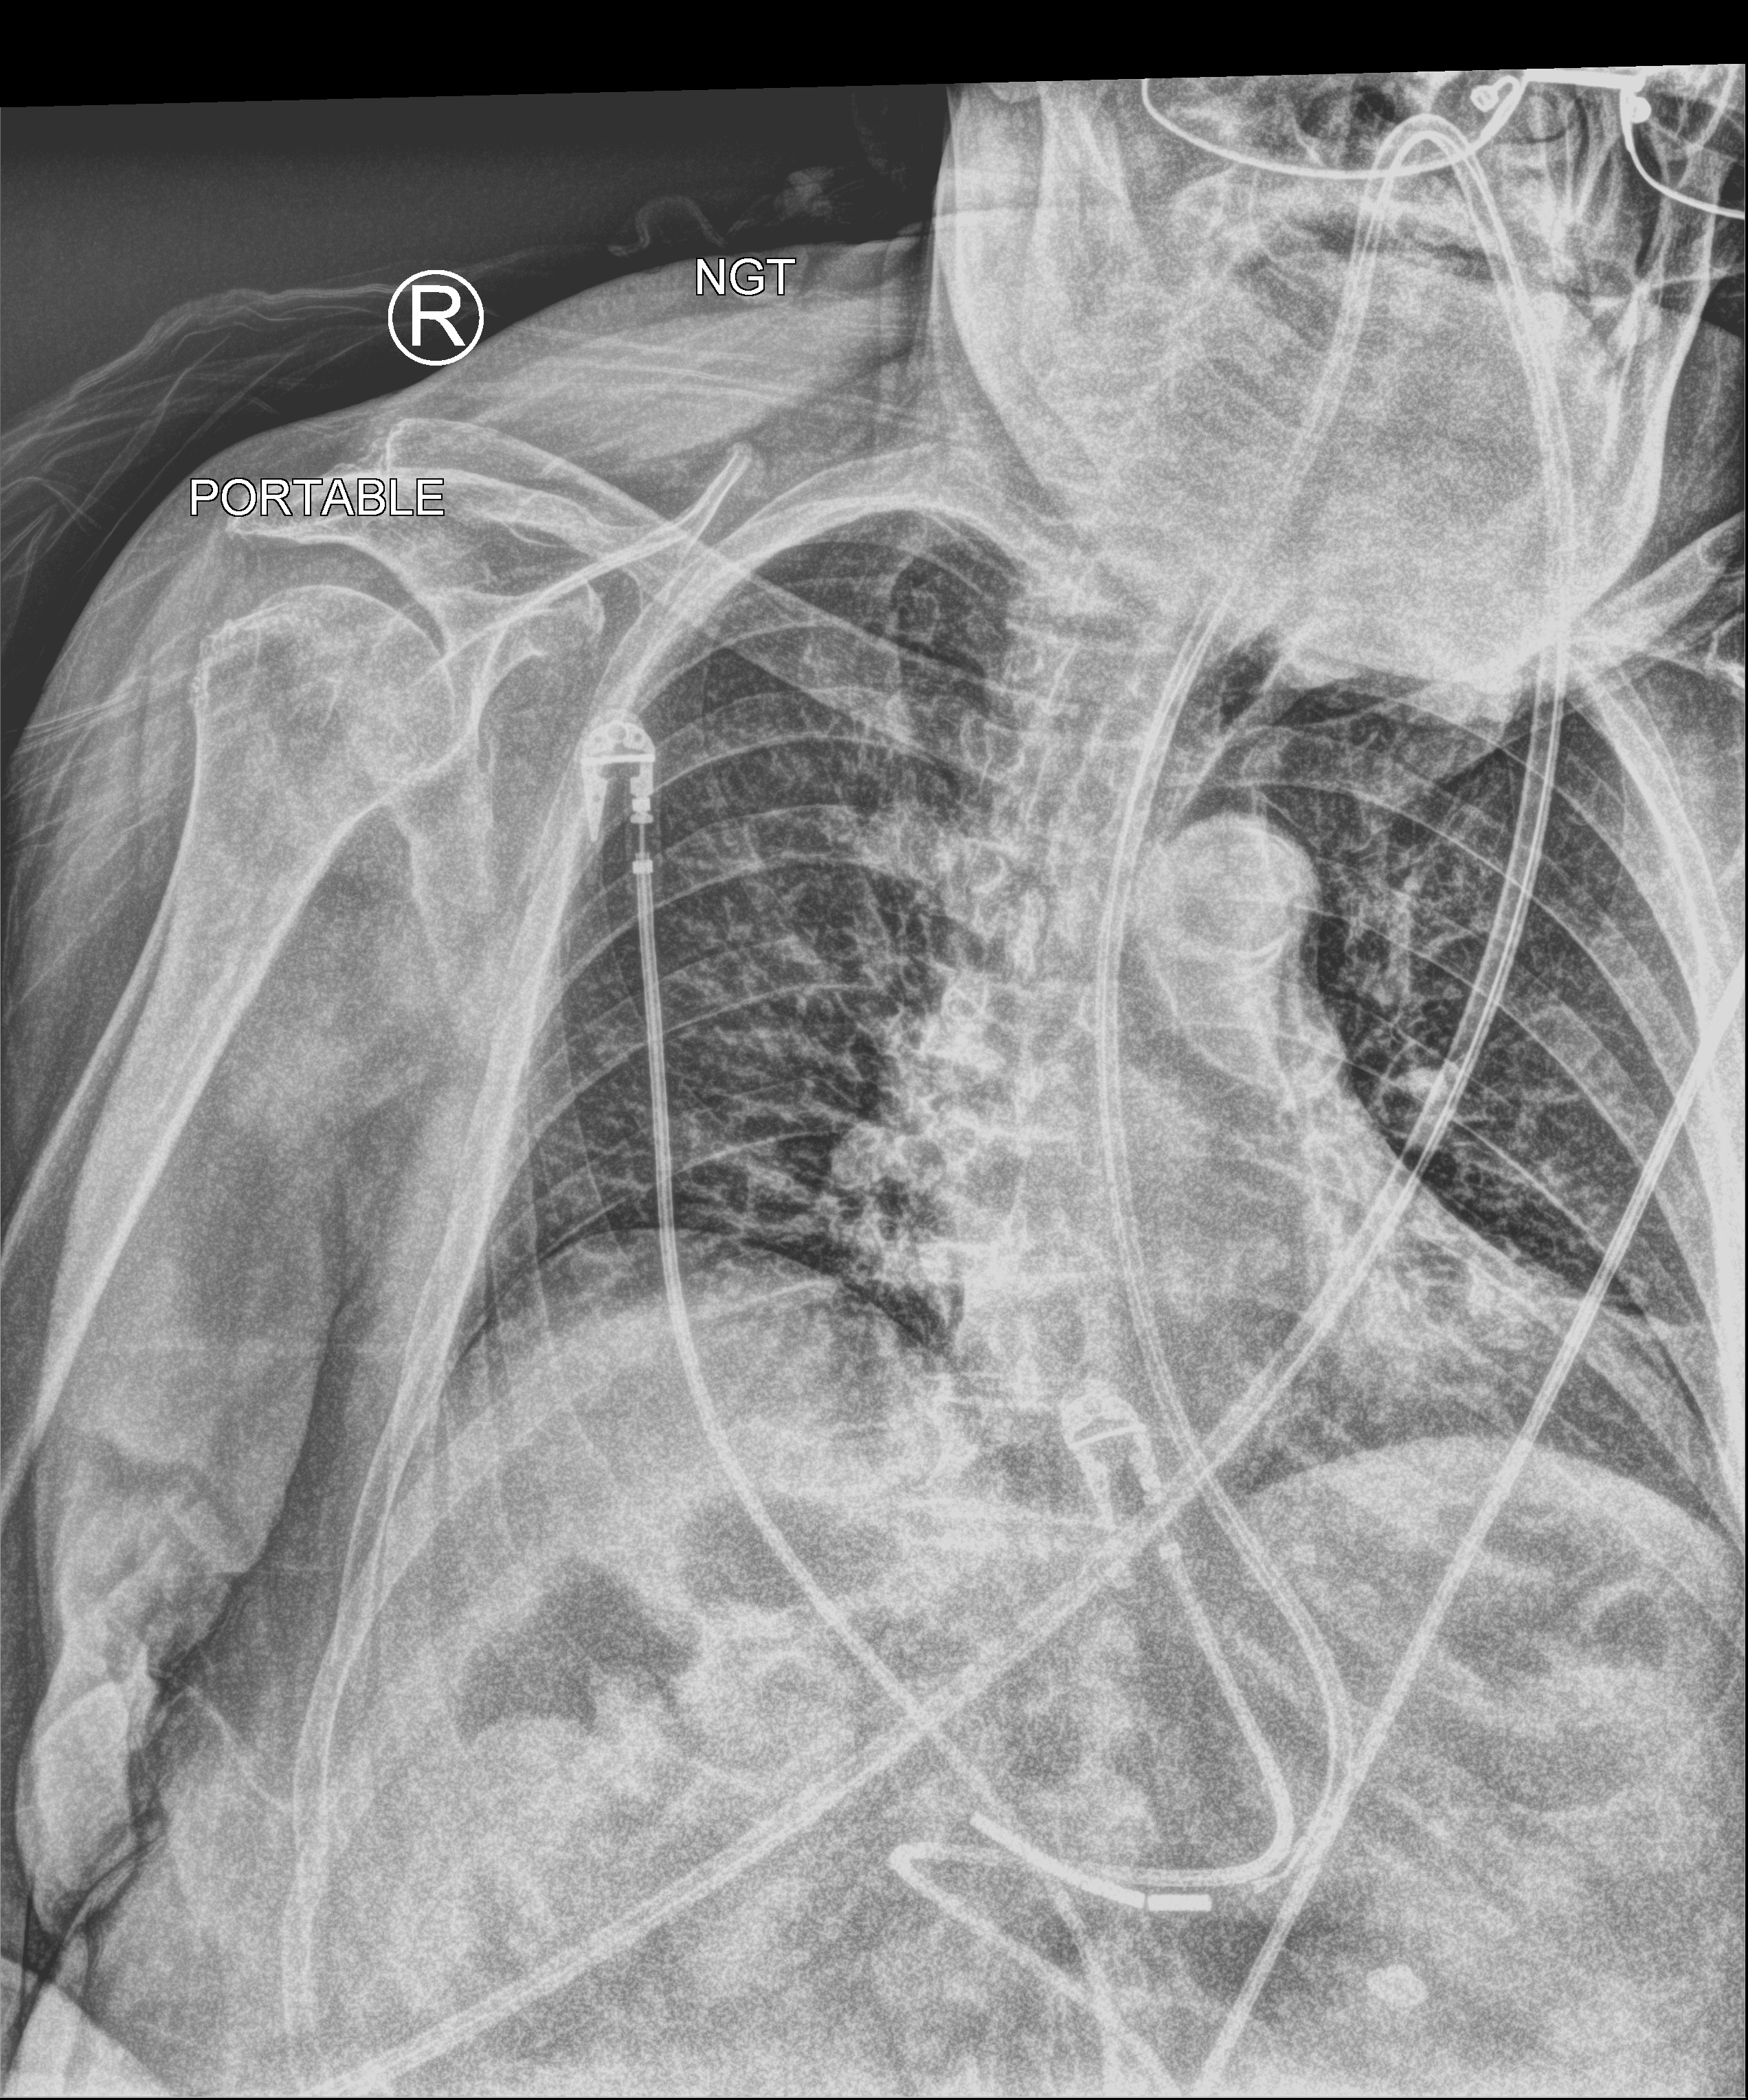
Bedside chest radiograph (computed radiography). Female patient hospitalised with COVID-19, age 75–90 years.
Hospital-stay facts (about this admission, not read from this image; timing relative to this image not recorded): mechanically ventilated during this hospital stay: no; length of hospital stay: 5 days.